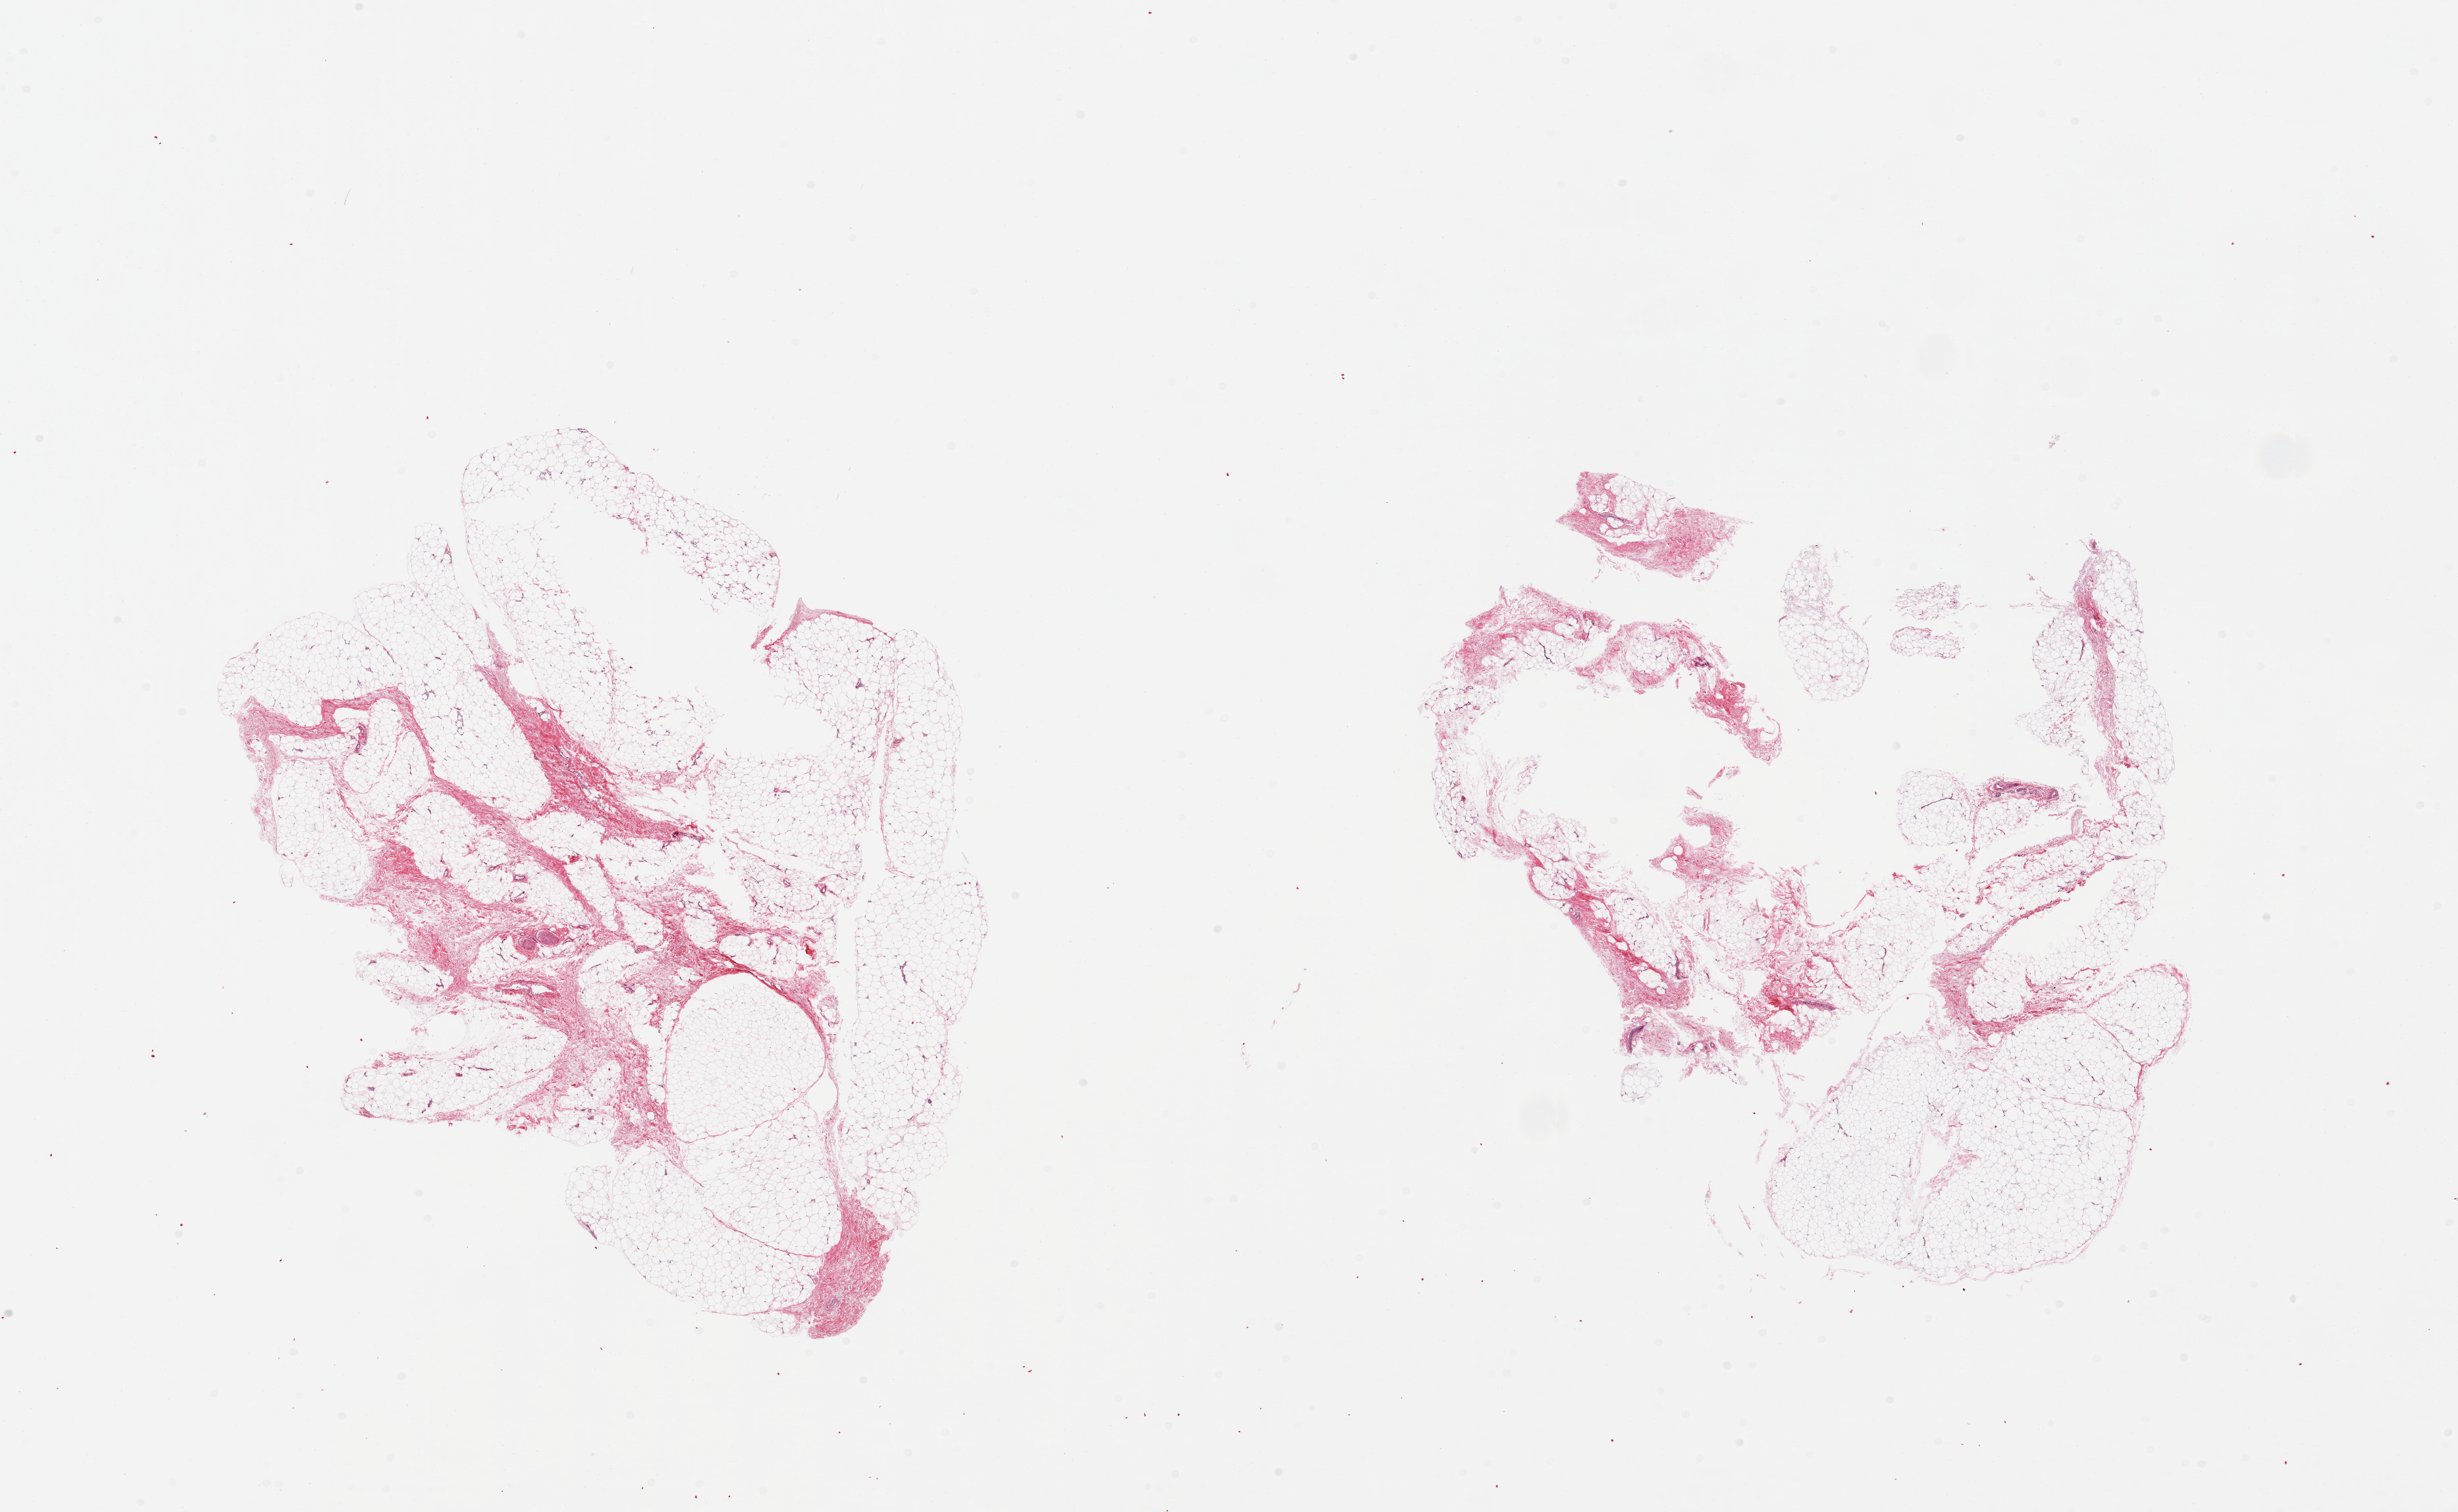
Whole-slide image, haematoxylin and eosin stain, brightfield, low-resolution overview of the scanned area, about 29.5 x 18.2 mm. PAXgene-fixed, paraffin-embedded tissue. Sampled site (target tissue): adipose tissue. Tissue donor sample. Male donor.
- reviewer comment on this tissue sample: 2 pieces; one piece is incomplete section (? fixation), up to ~30% fibrous/nerve tissue